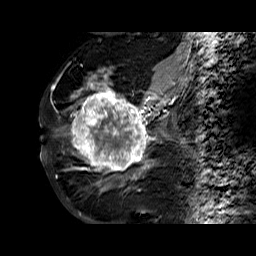
Breast MRI (dynamic contrast-enhanced), one sagittal slice; position 32 of 60 along the scan axis; dynamic contrast-enhanced series, time point 2 of 6 at this slice position (early post-contrast); 1.5 T; TE 6.3 ms, TR 32.4 ms; 4 mm slice thickness; 256 × 256 image matrix, field of view 200 × 200 mm. Female patient. From the clinical record (not read from this slice): setting: breast cancer imaged before/during neoadjuvant chemotherapy; receptor status: HR-positive, HER2-negative.
Structures marked on this image (semi-automatic segmentation, software-assisted and operator-edited):
- analysis volume of interest (the breast-tissue region the enhancement analysis was run in; not a lesion): bounding box (x1, y1, x2, y2) in pixels: (68, 72, 177, 180)
- tumour enhancement mask (voxels above the 100 % enhancement threshold inside the analysis volume of interest): (71, 75, 174, 180)